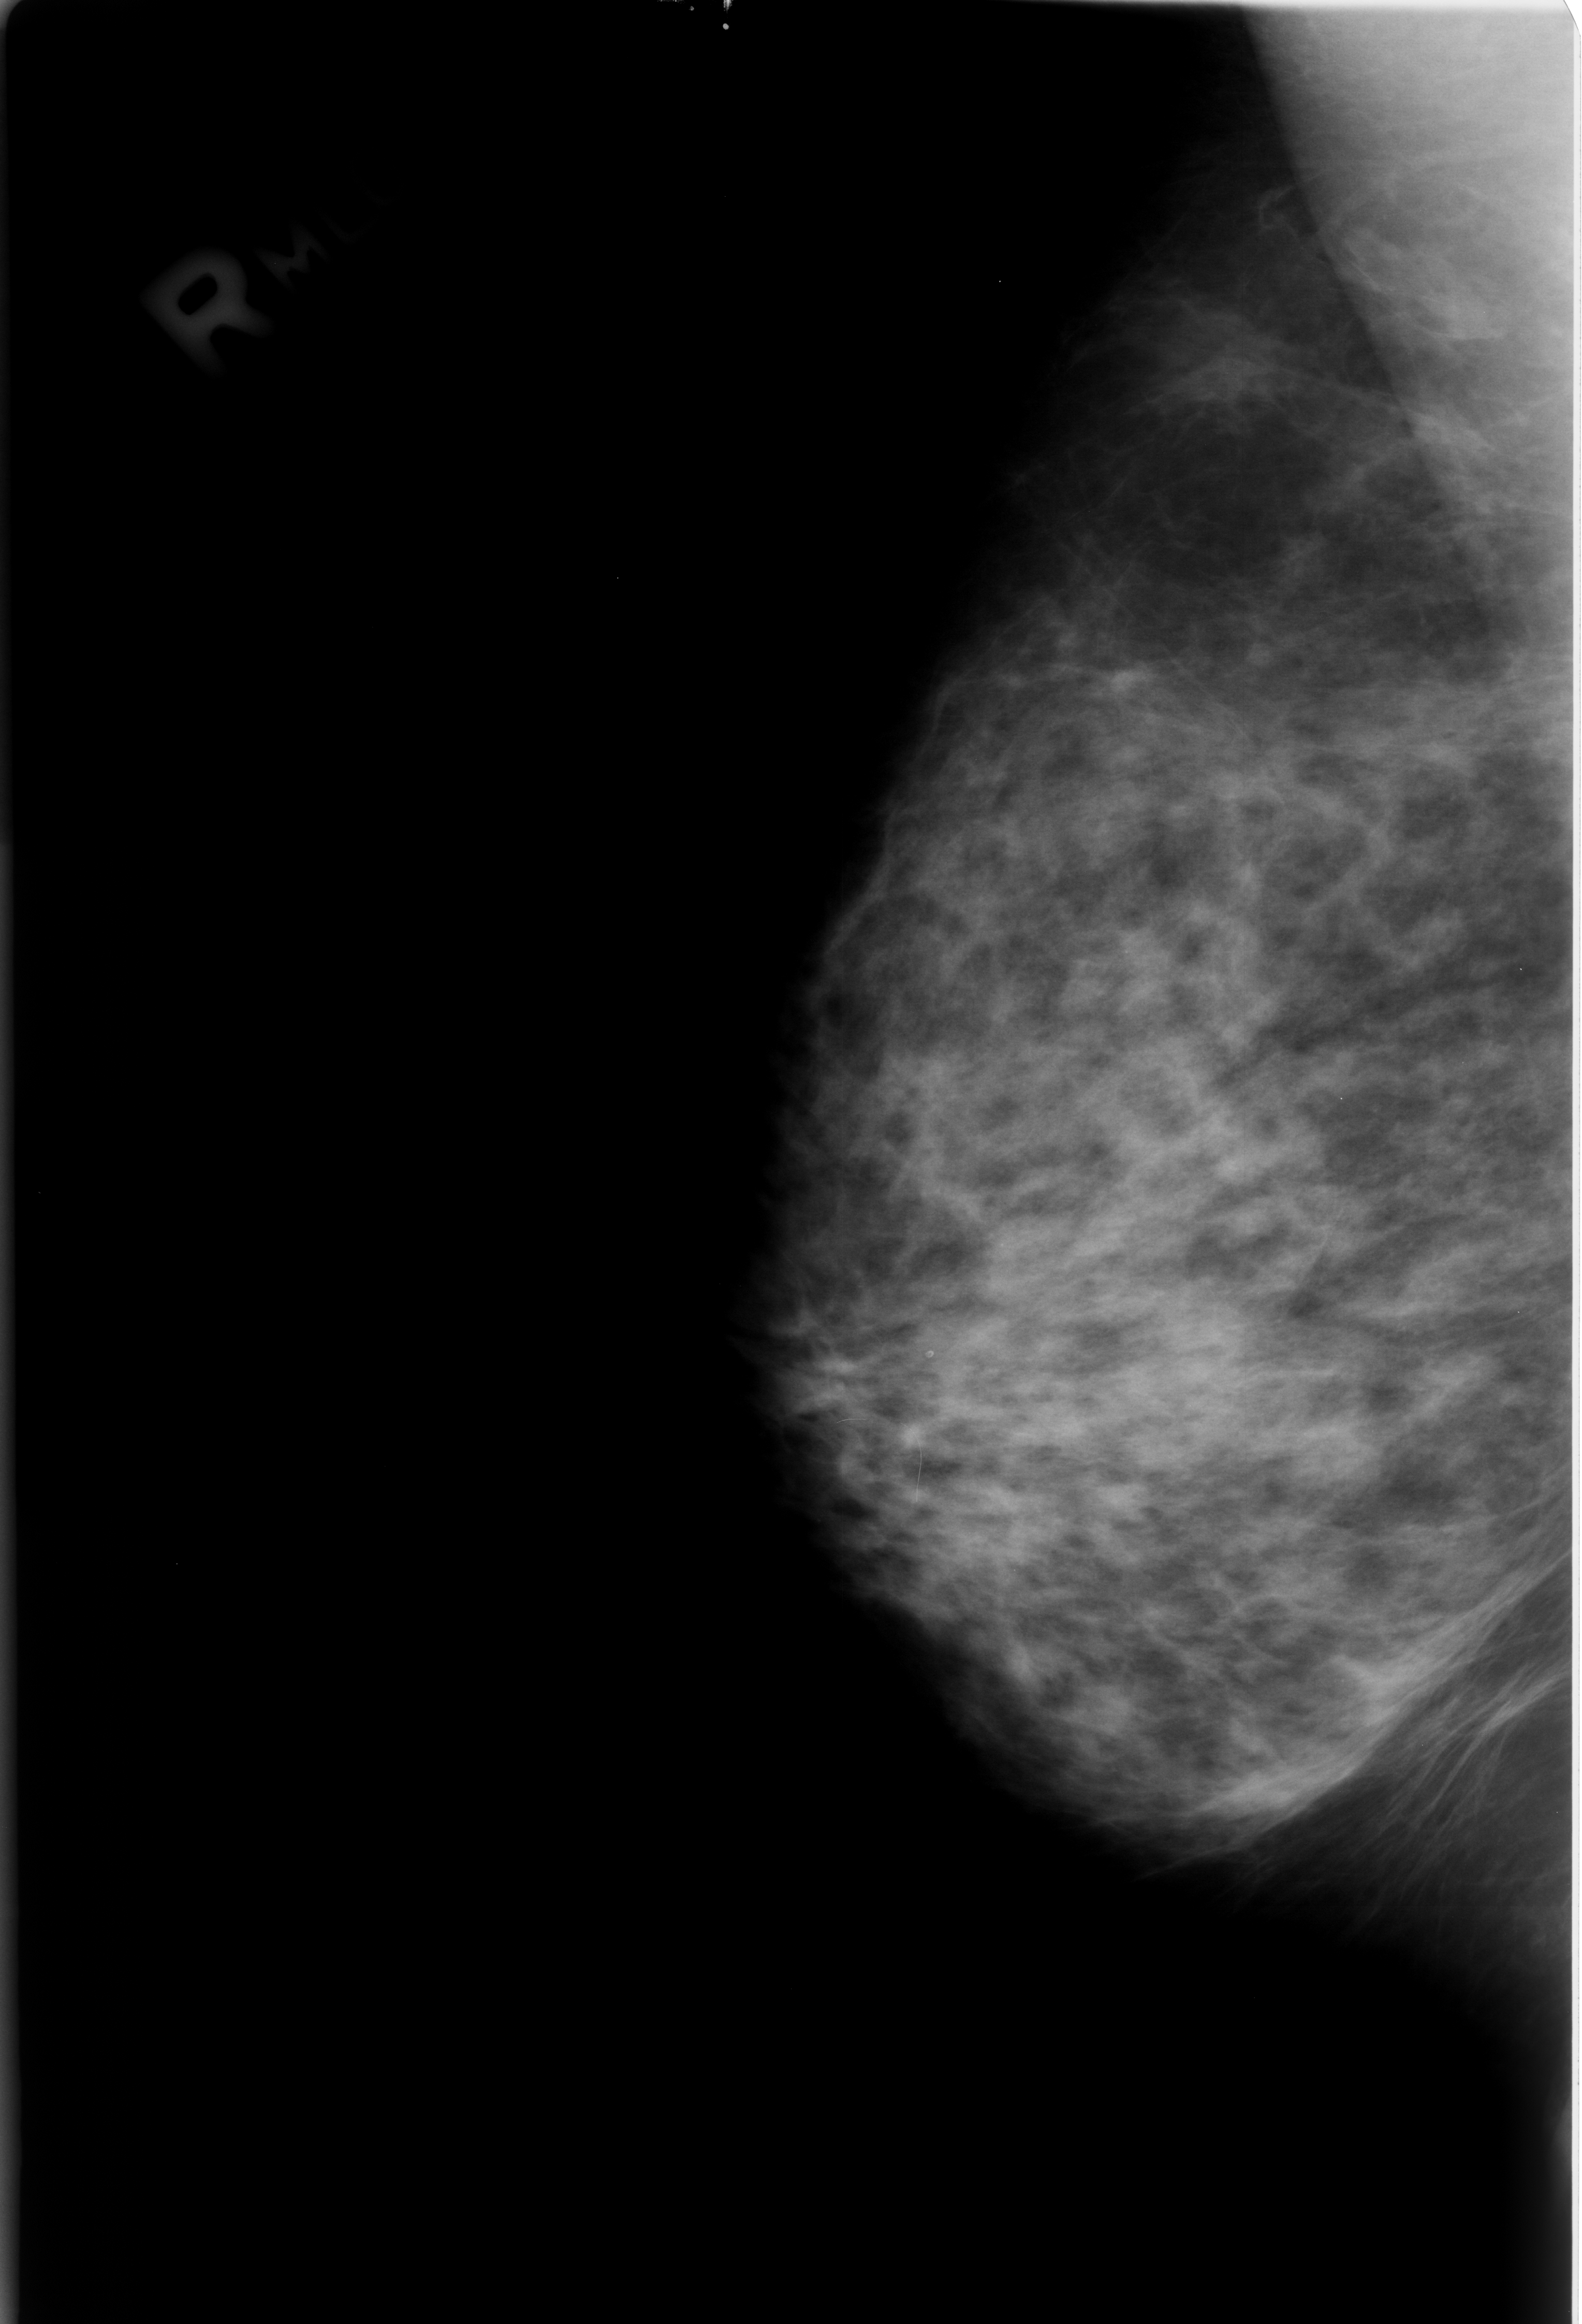
Scanned film-screen mammogram; right breast; MLO view; BI-RADS breast density category 4 (scale 1–4); 1582 × 2324 image matrix.
Expert-marked regions of interest on this image (one box per marked abnormality):
- calcifications, morphology lucent center; BI-RADS assessment category 2; subtlety rating 3 on a 1 (subtle) to 5 (obvious) scale; benign; no additional work-up was recommended (outcome (as recorded, no biopsy): benign without callback): bounding box [x1, y1, x2, y2] px = [915, 1342, 945, 1368]